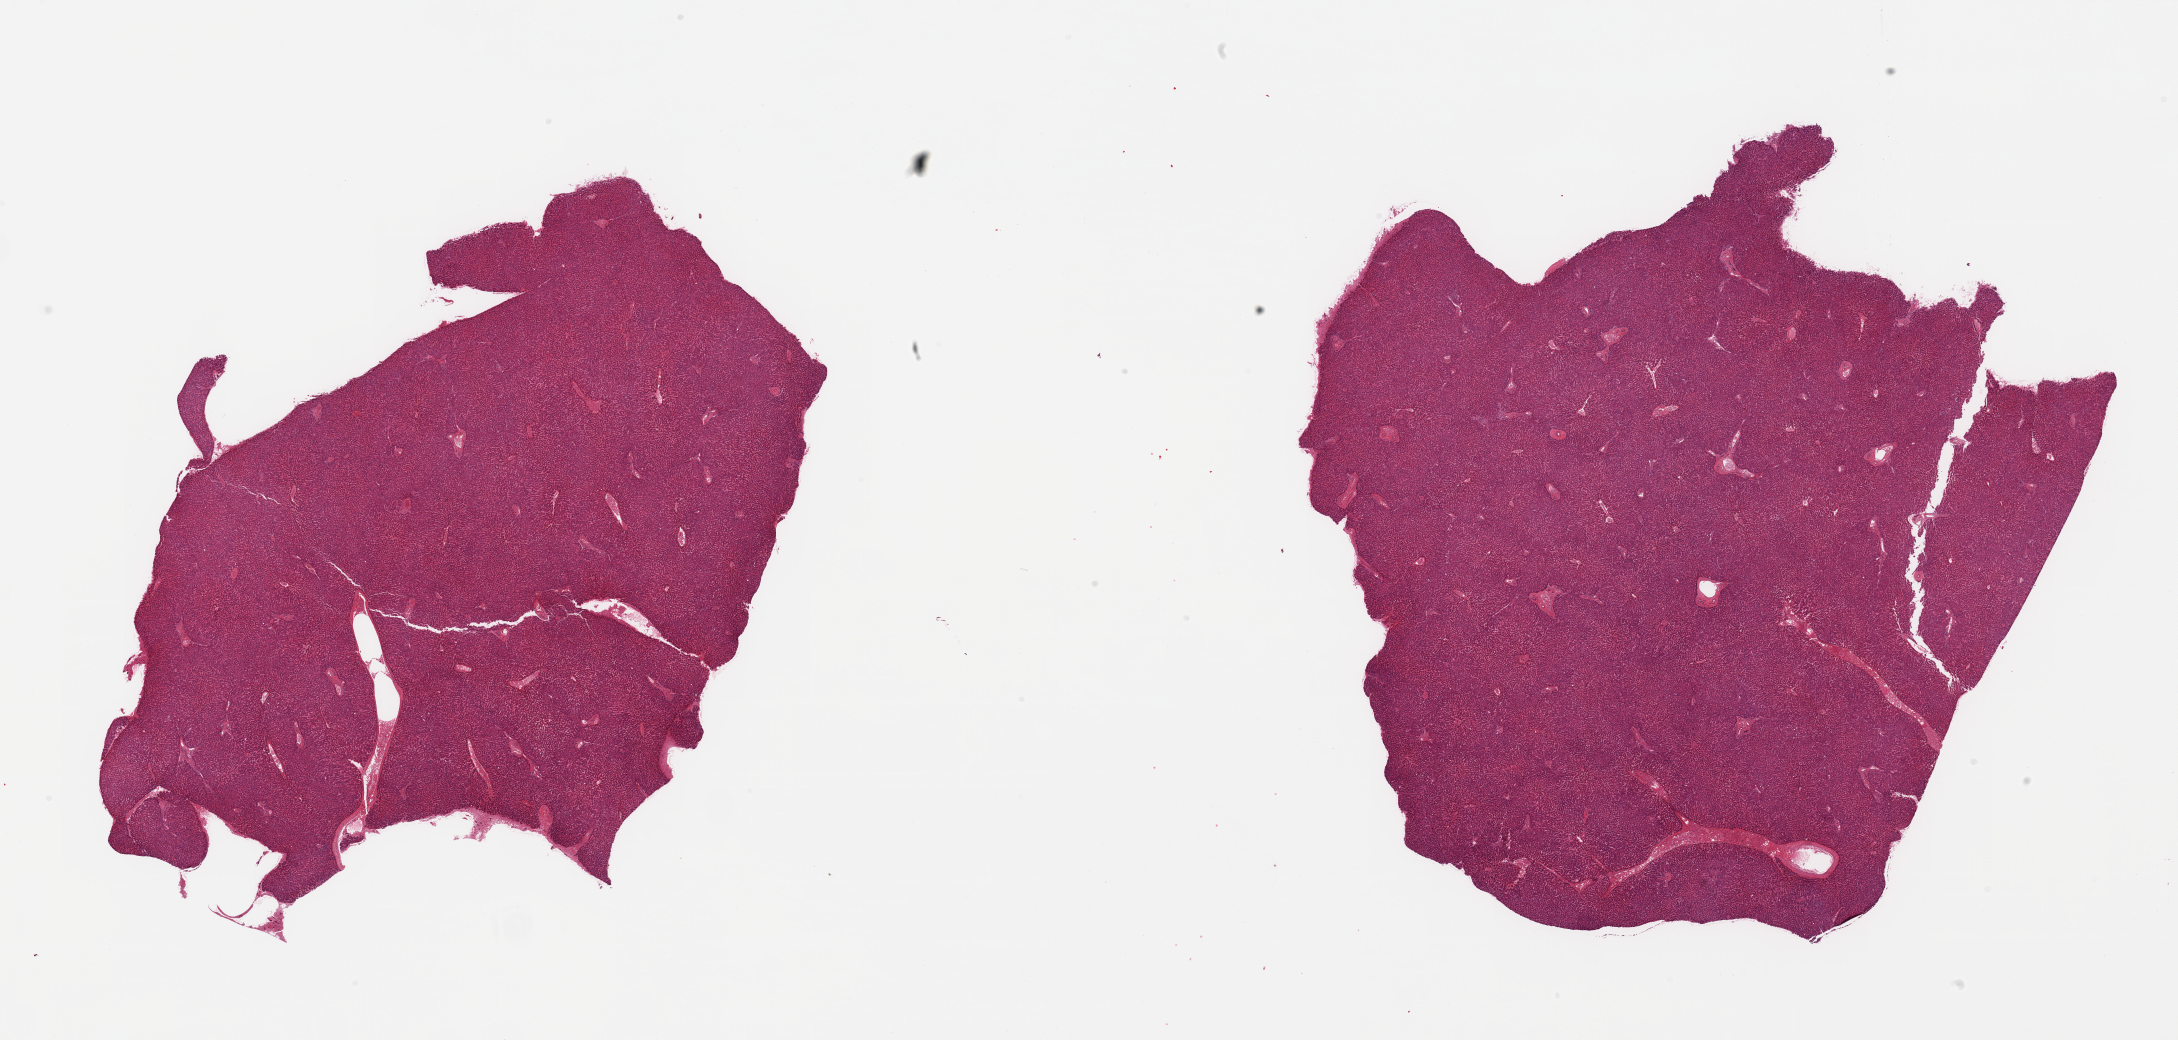
Hematoxylin and eosin (H&E) whole-slide image — low-resolution overview of the scanned area, about 34.5 x 16.5 mm. PAXgene-fixed, paraffin-embedded tissue. Sampled site (target tissue): liver. Tissue donor sample. Male donor.
Pathologist's review note for this sample: 2 pieces; some congestion.